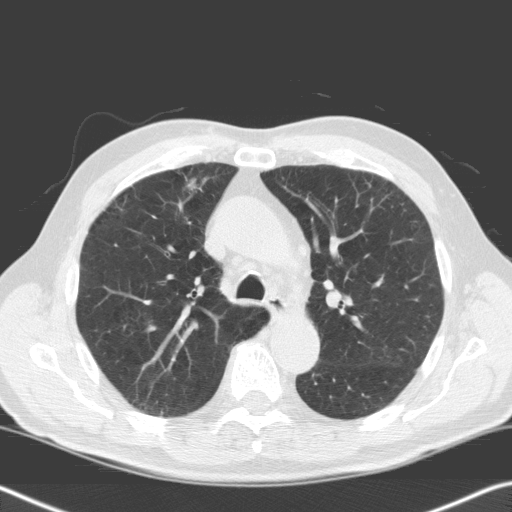
Low-dose screening chest CT, axial slice. First (baseline) screen. Lung window (W 1500 / L -600 HU). 3.2 mm slice thickness. Standard (soft-tissue) reconstruction kernel (C). 120 kVp. Male participant, aged 68 years at enrolment. Current smoker at enrolment.
Lesion marked by an expert reader, bounding box (x1, y1, x2, y2) in pixels: (169, 168, 217, 217). The exam's reader record, not a measurement of the box and not confirmed to be the same lesion: non-calcified nodule or mass ≥4 mm, right upper lobe, 18 × 12 mm, spiculated (stellate) margins, soft tissue attenuation. Official screen result: positive, change unspecified: nodule(s) >= 4 mm or enlarging nodule(s), mass(es), or other non-specific abnormalities suspicious for lung cancer. Lung cancer was diagnosed 73 days after this screen: squamous cell carcinoma, NOS, right upper lobe, moderately differentiated (G2), stage IIIA (AJCC 6th edition), 7 mm at pathology.